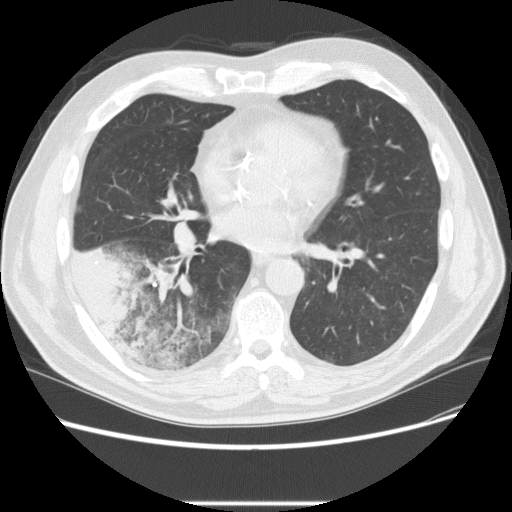
Low-dose screening chest CT, one axial slice. Slice 103 of 233 in the series (ordered by position). 120 kVp. Lung window (W 1500 / L -600 HU). 2.5 mm slice thickness. 512 × 512 image matrix.
Annotated regions visible in this slice (manually delineated by an expert):
- lesion 3 (tumor, lower lobe of right lung): bounding box (x1, y1, x2, y2) in pixels: (71, 245, 134, 341)